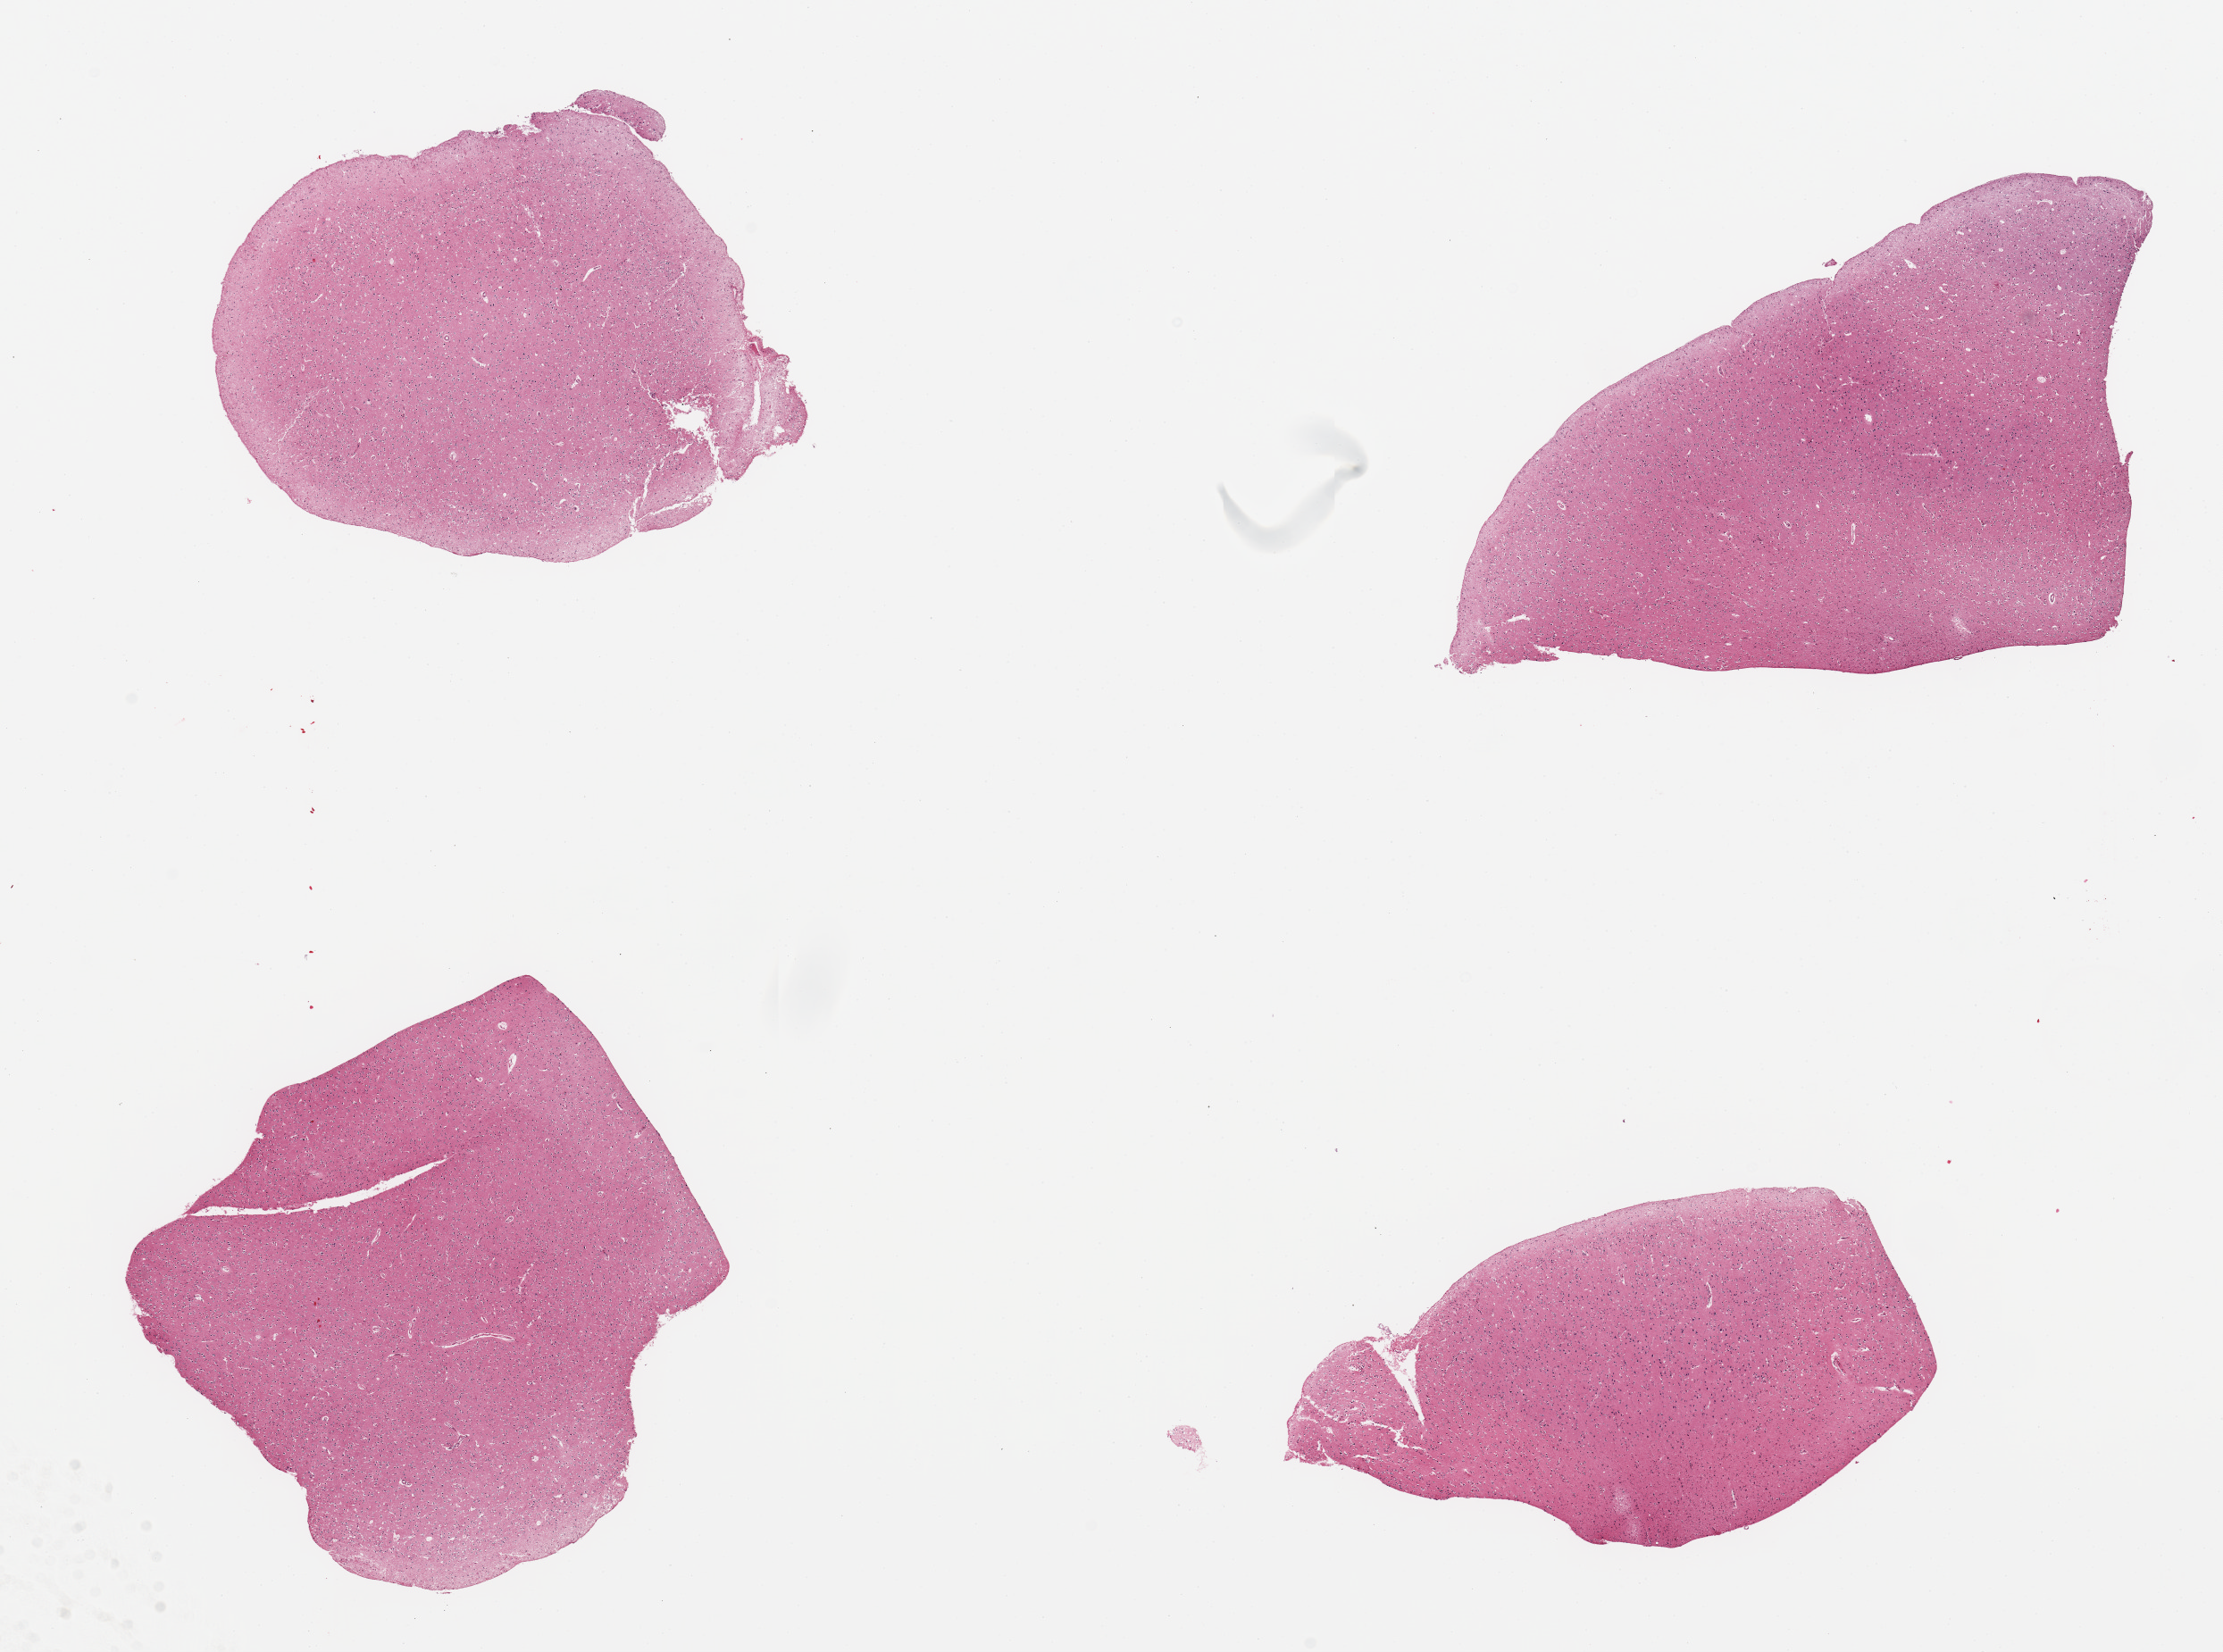
Digitized haematoxylin and eosin-stained section, low-resolution overview of the scanned area, about 19.7 x 14.6 mm, PAXgene-fixed, paraffin-embedded tissue, section of cerebral cortex (target tissue), donor tissue sample.
Pathologist's review note for this sample: pieces.